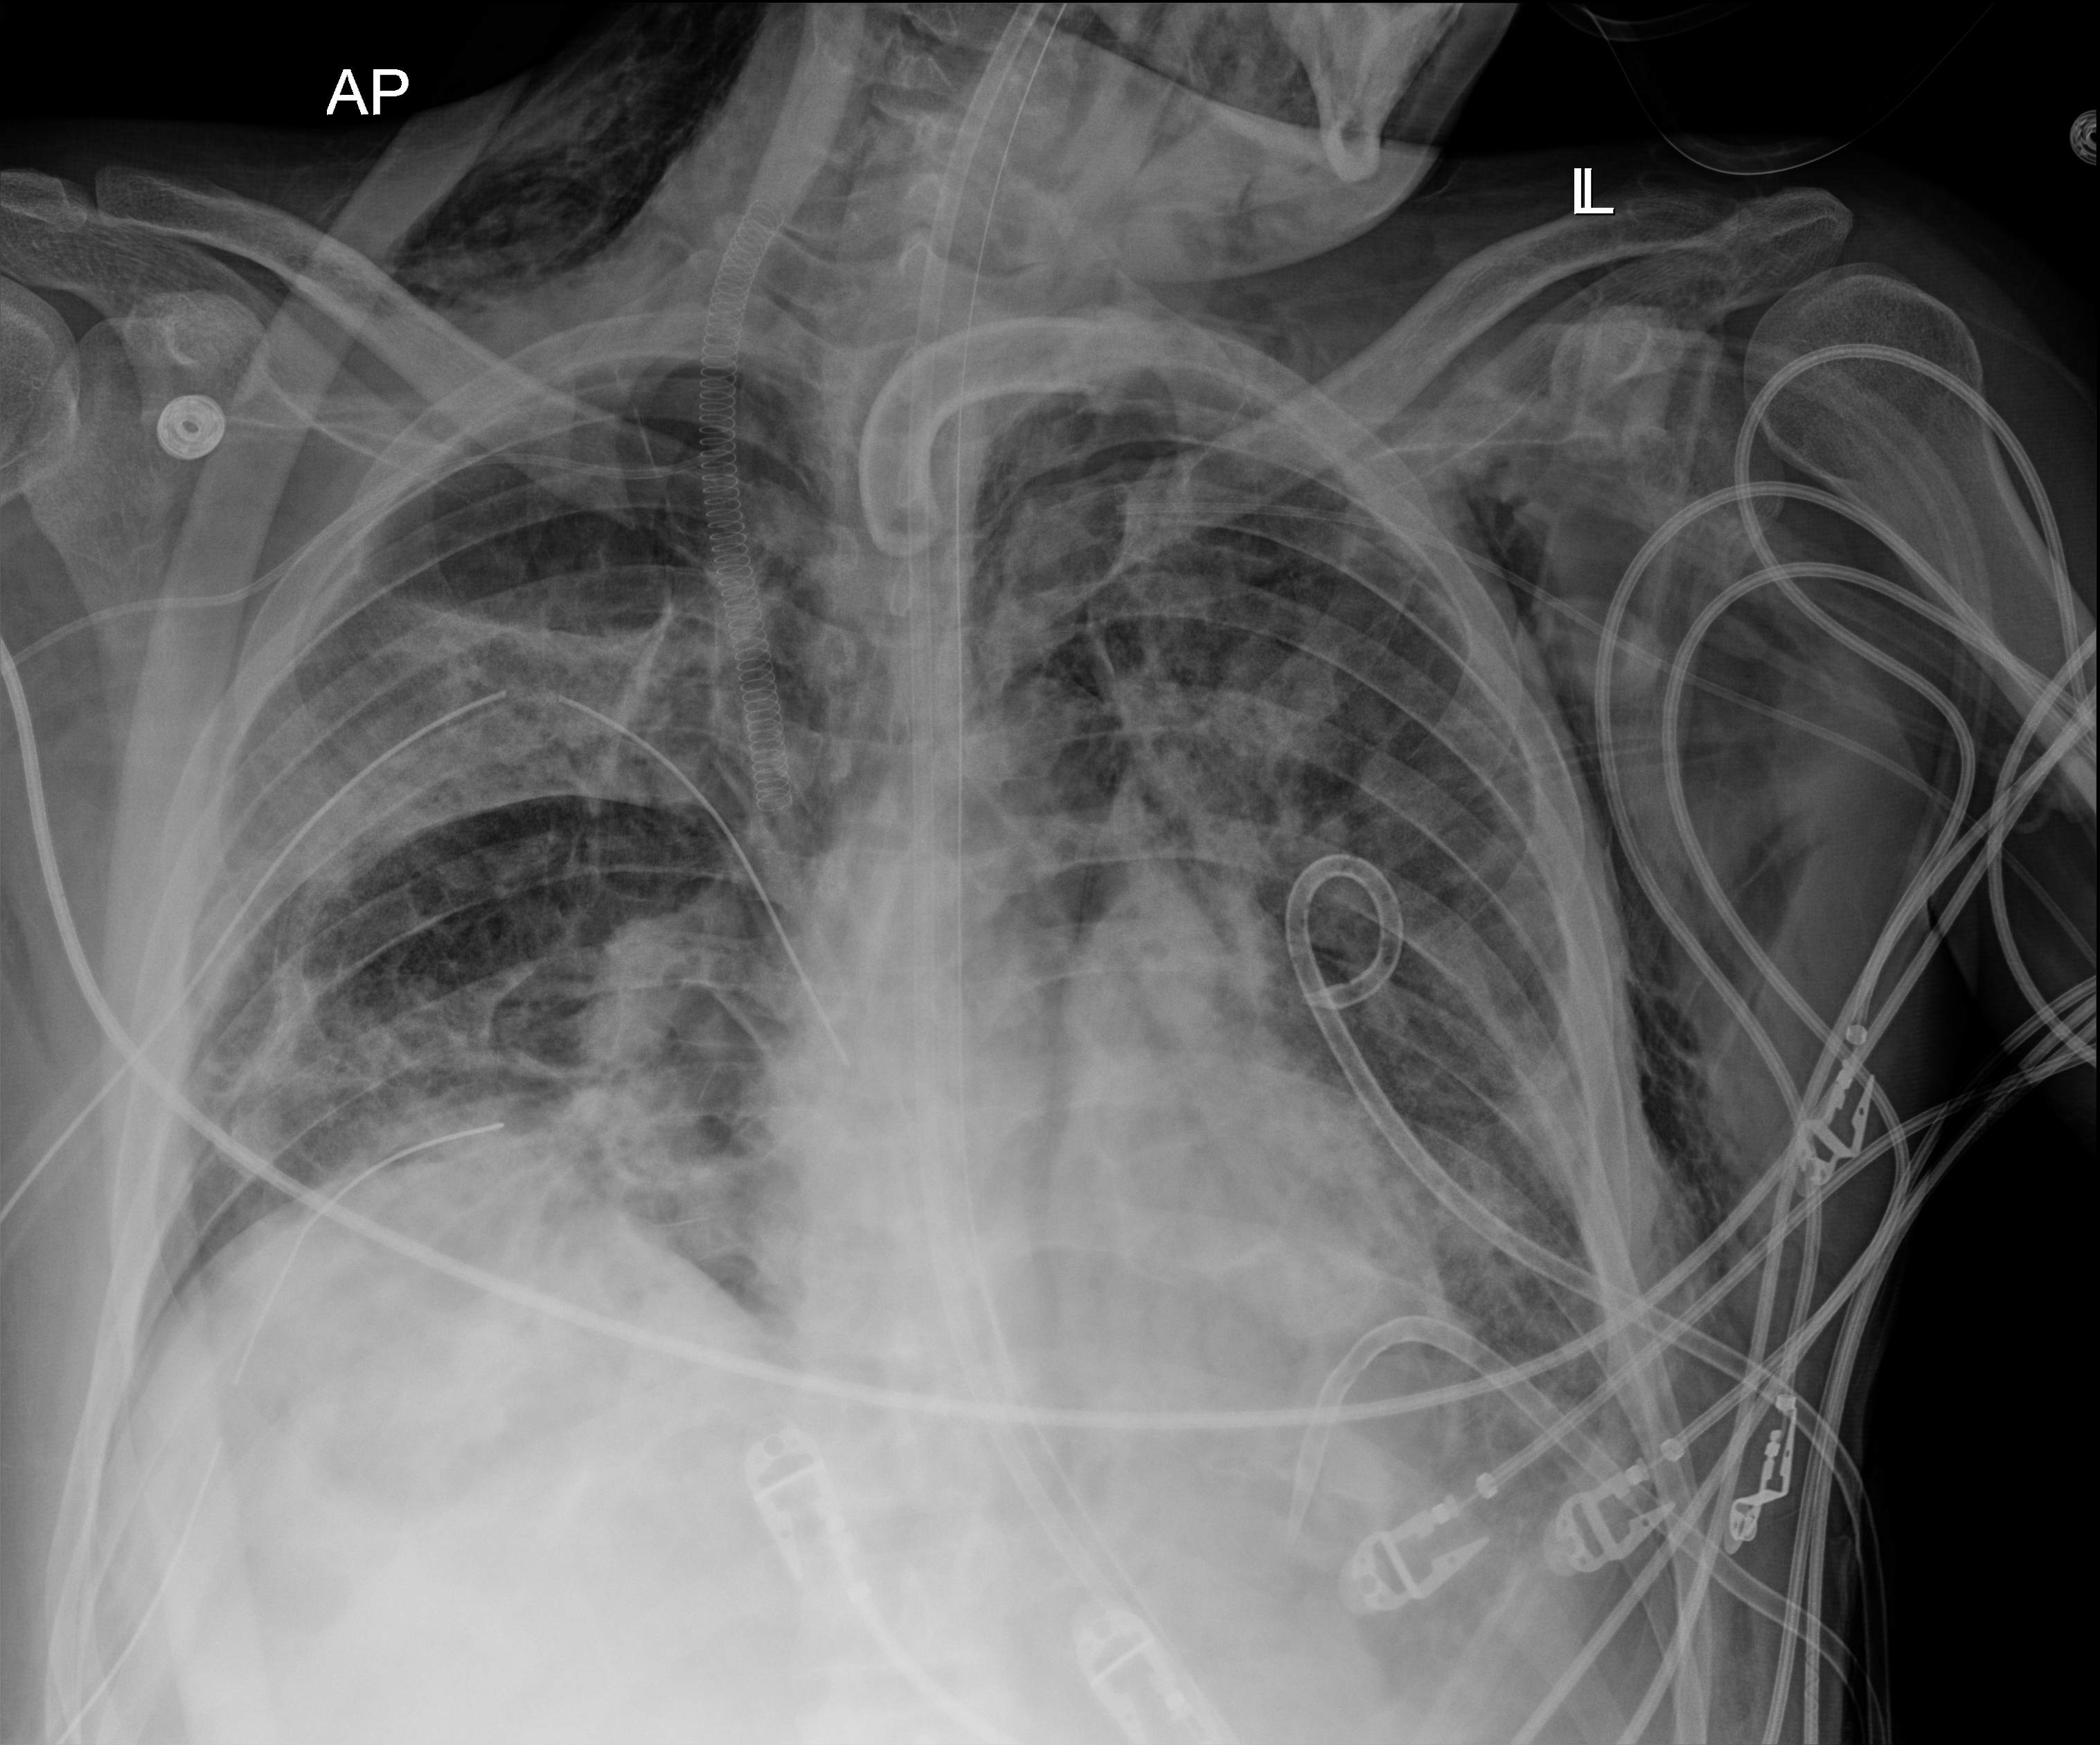
Chest radiograph. Patient hospitalised with COVID-19, aged 18–59 years.
From the hospital-stay record, not from the radiograph (when in the stay this image was taken is not recorded): diabetes (admission record): no.